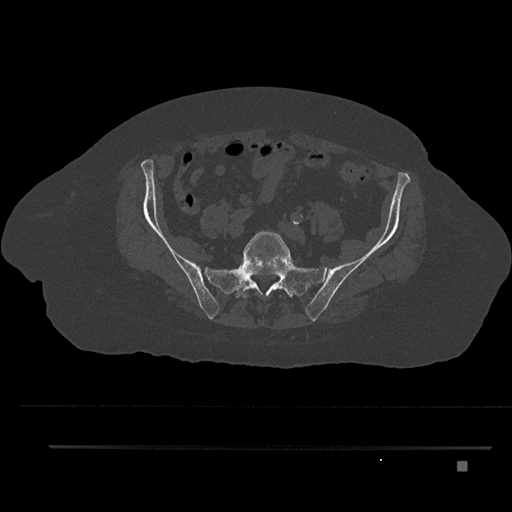
CT including the spine, one axial slice; position 15 of 797 along the scan axis; reconstruction kernel Br40s/3; bone window (W 1800 / L 400 HU); 0.5 mm slice thickness; 512 × 512 image matrix, field of view 437 × 437 mm. Patient: female, 76 years. Case-level facts recorded for this patient, not image findings: primary cancer: lung; vertebrae with lytic lesions (as recorded): T11, L3.
Structures marked on this image (semi-automatic segmentation, software-assisted and operator-edited):
- L5 vertebra: box from (x=242, y=231) to (x=290, y=298) px